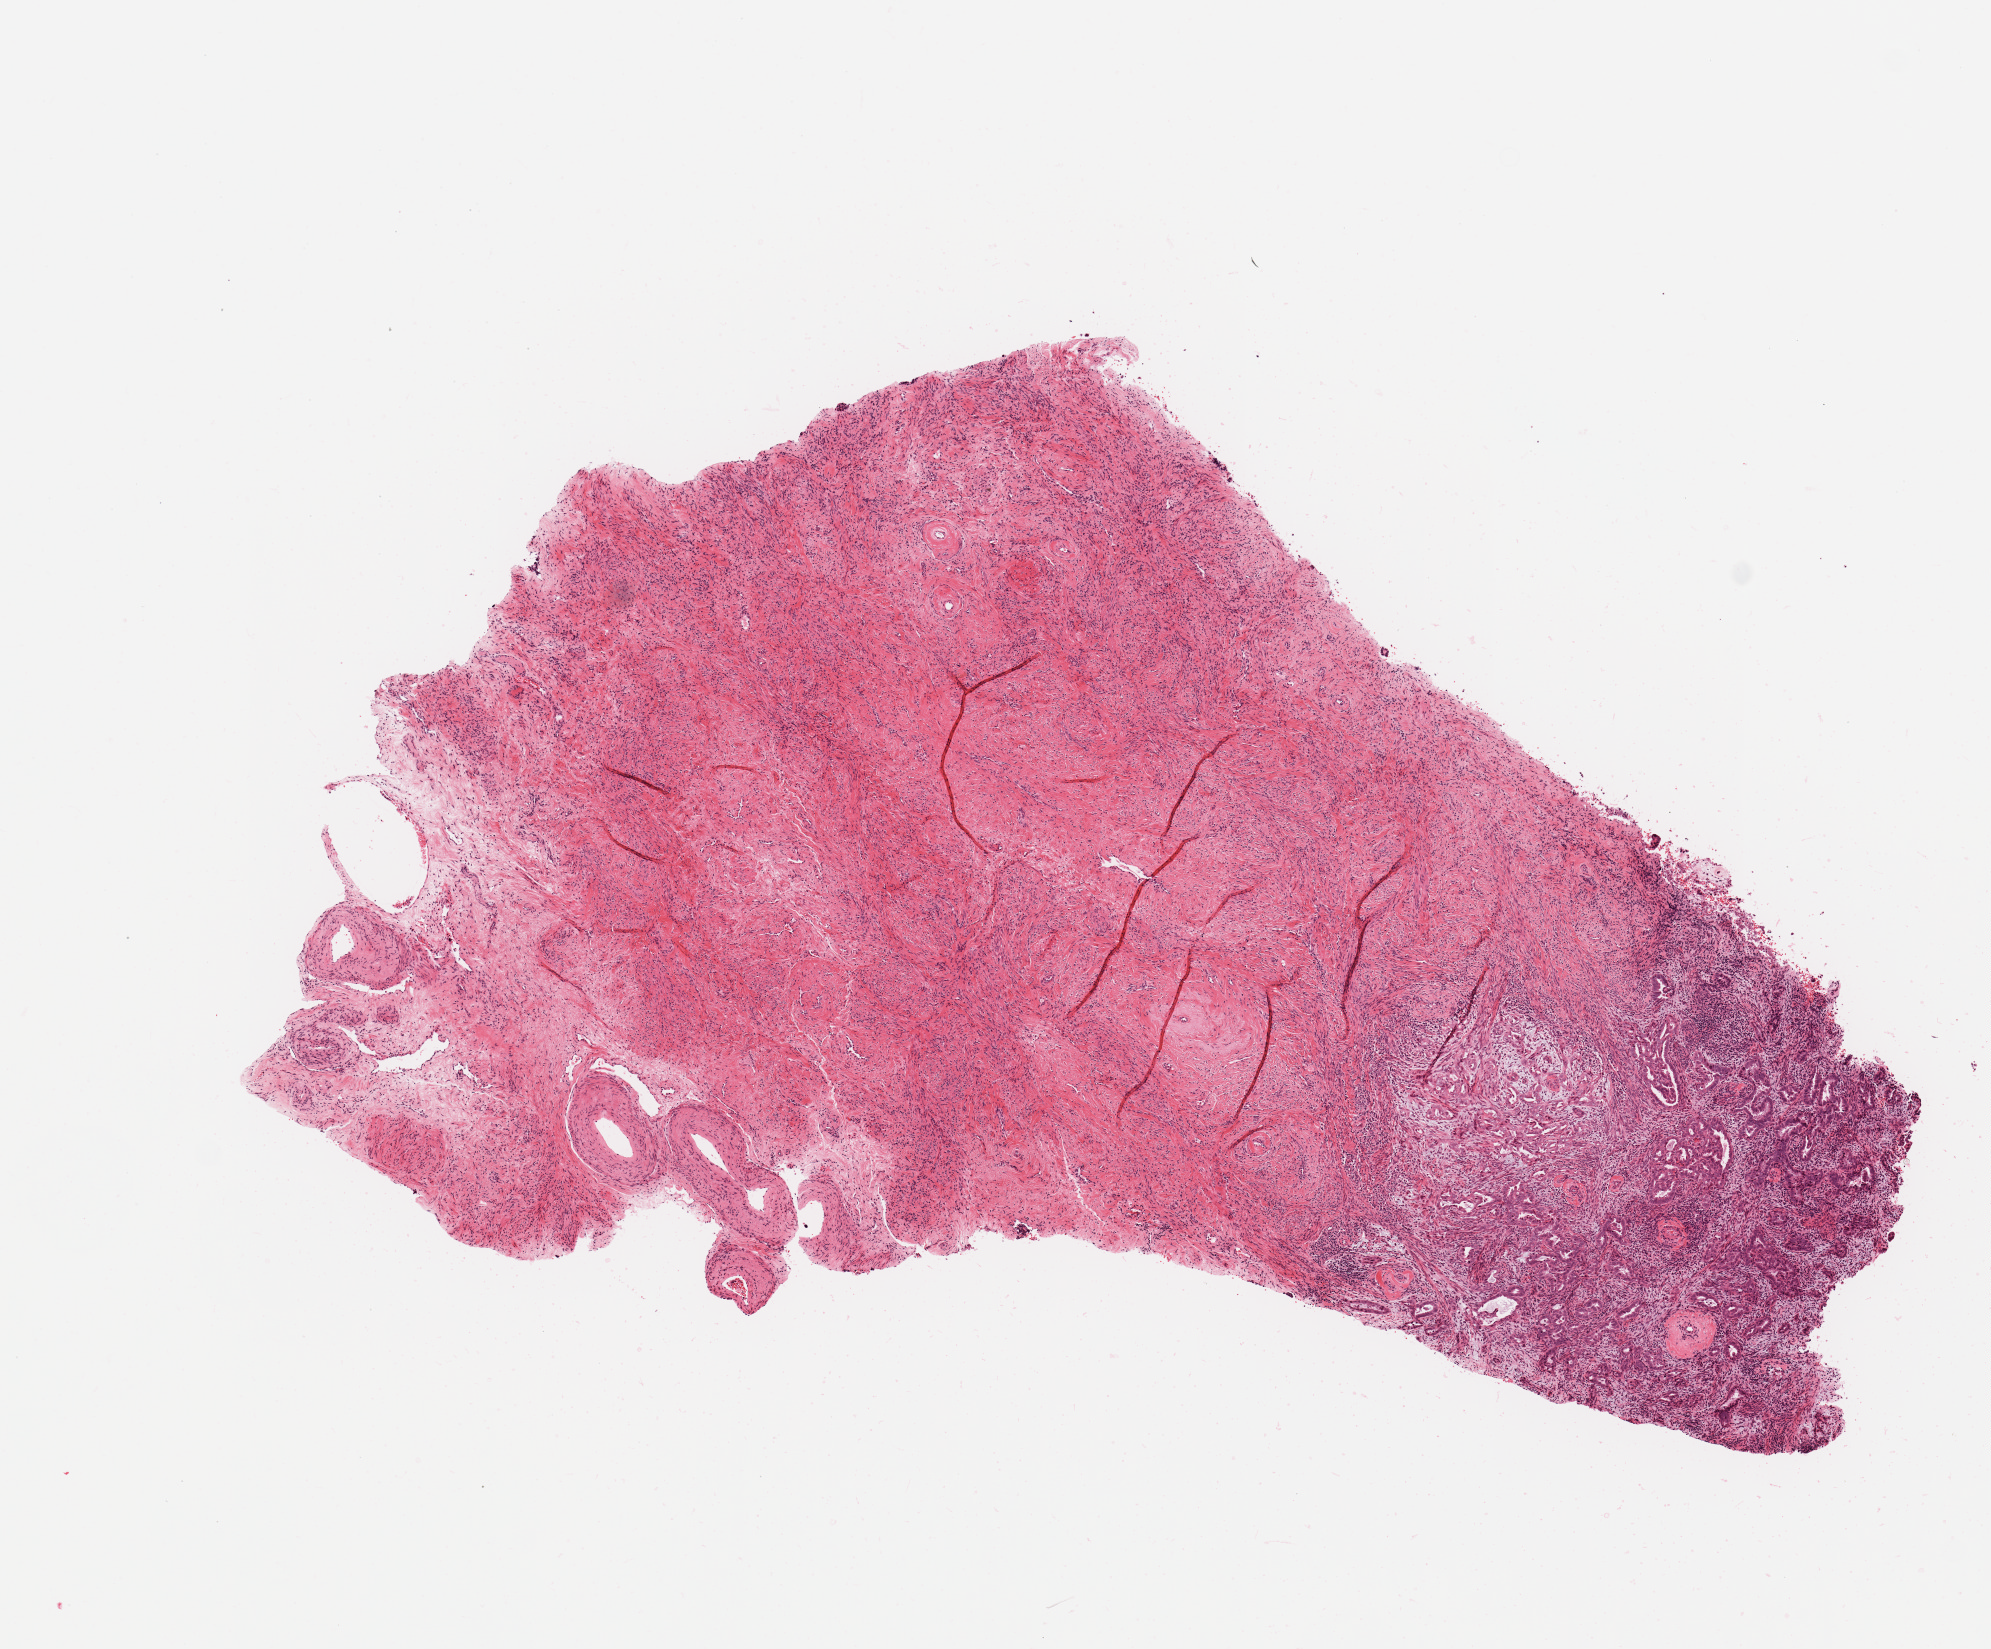
H&E whole-slide image — a low-resolution overview of the entire scanned area, about 7.9 x 6.5 mm (acquisition: 20x scan); uterus, normal (non-tumour) tissue. Patient: female, age 73 years.
This section: normal (non-tumour) tissue from the same patient. Patient diagnosis: Endometrioid adenocarcinoma, NOS.